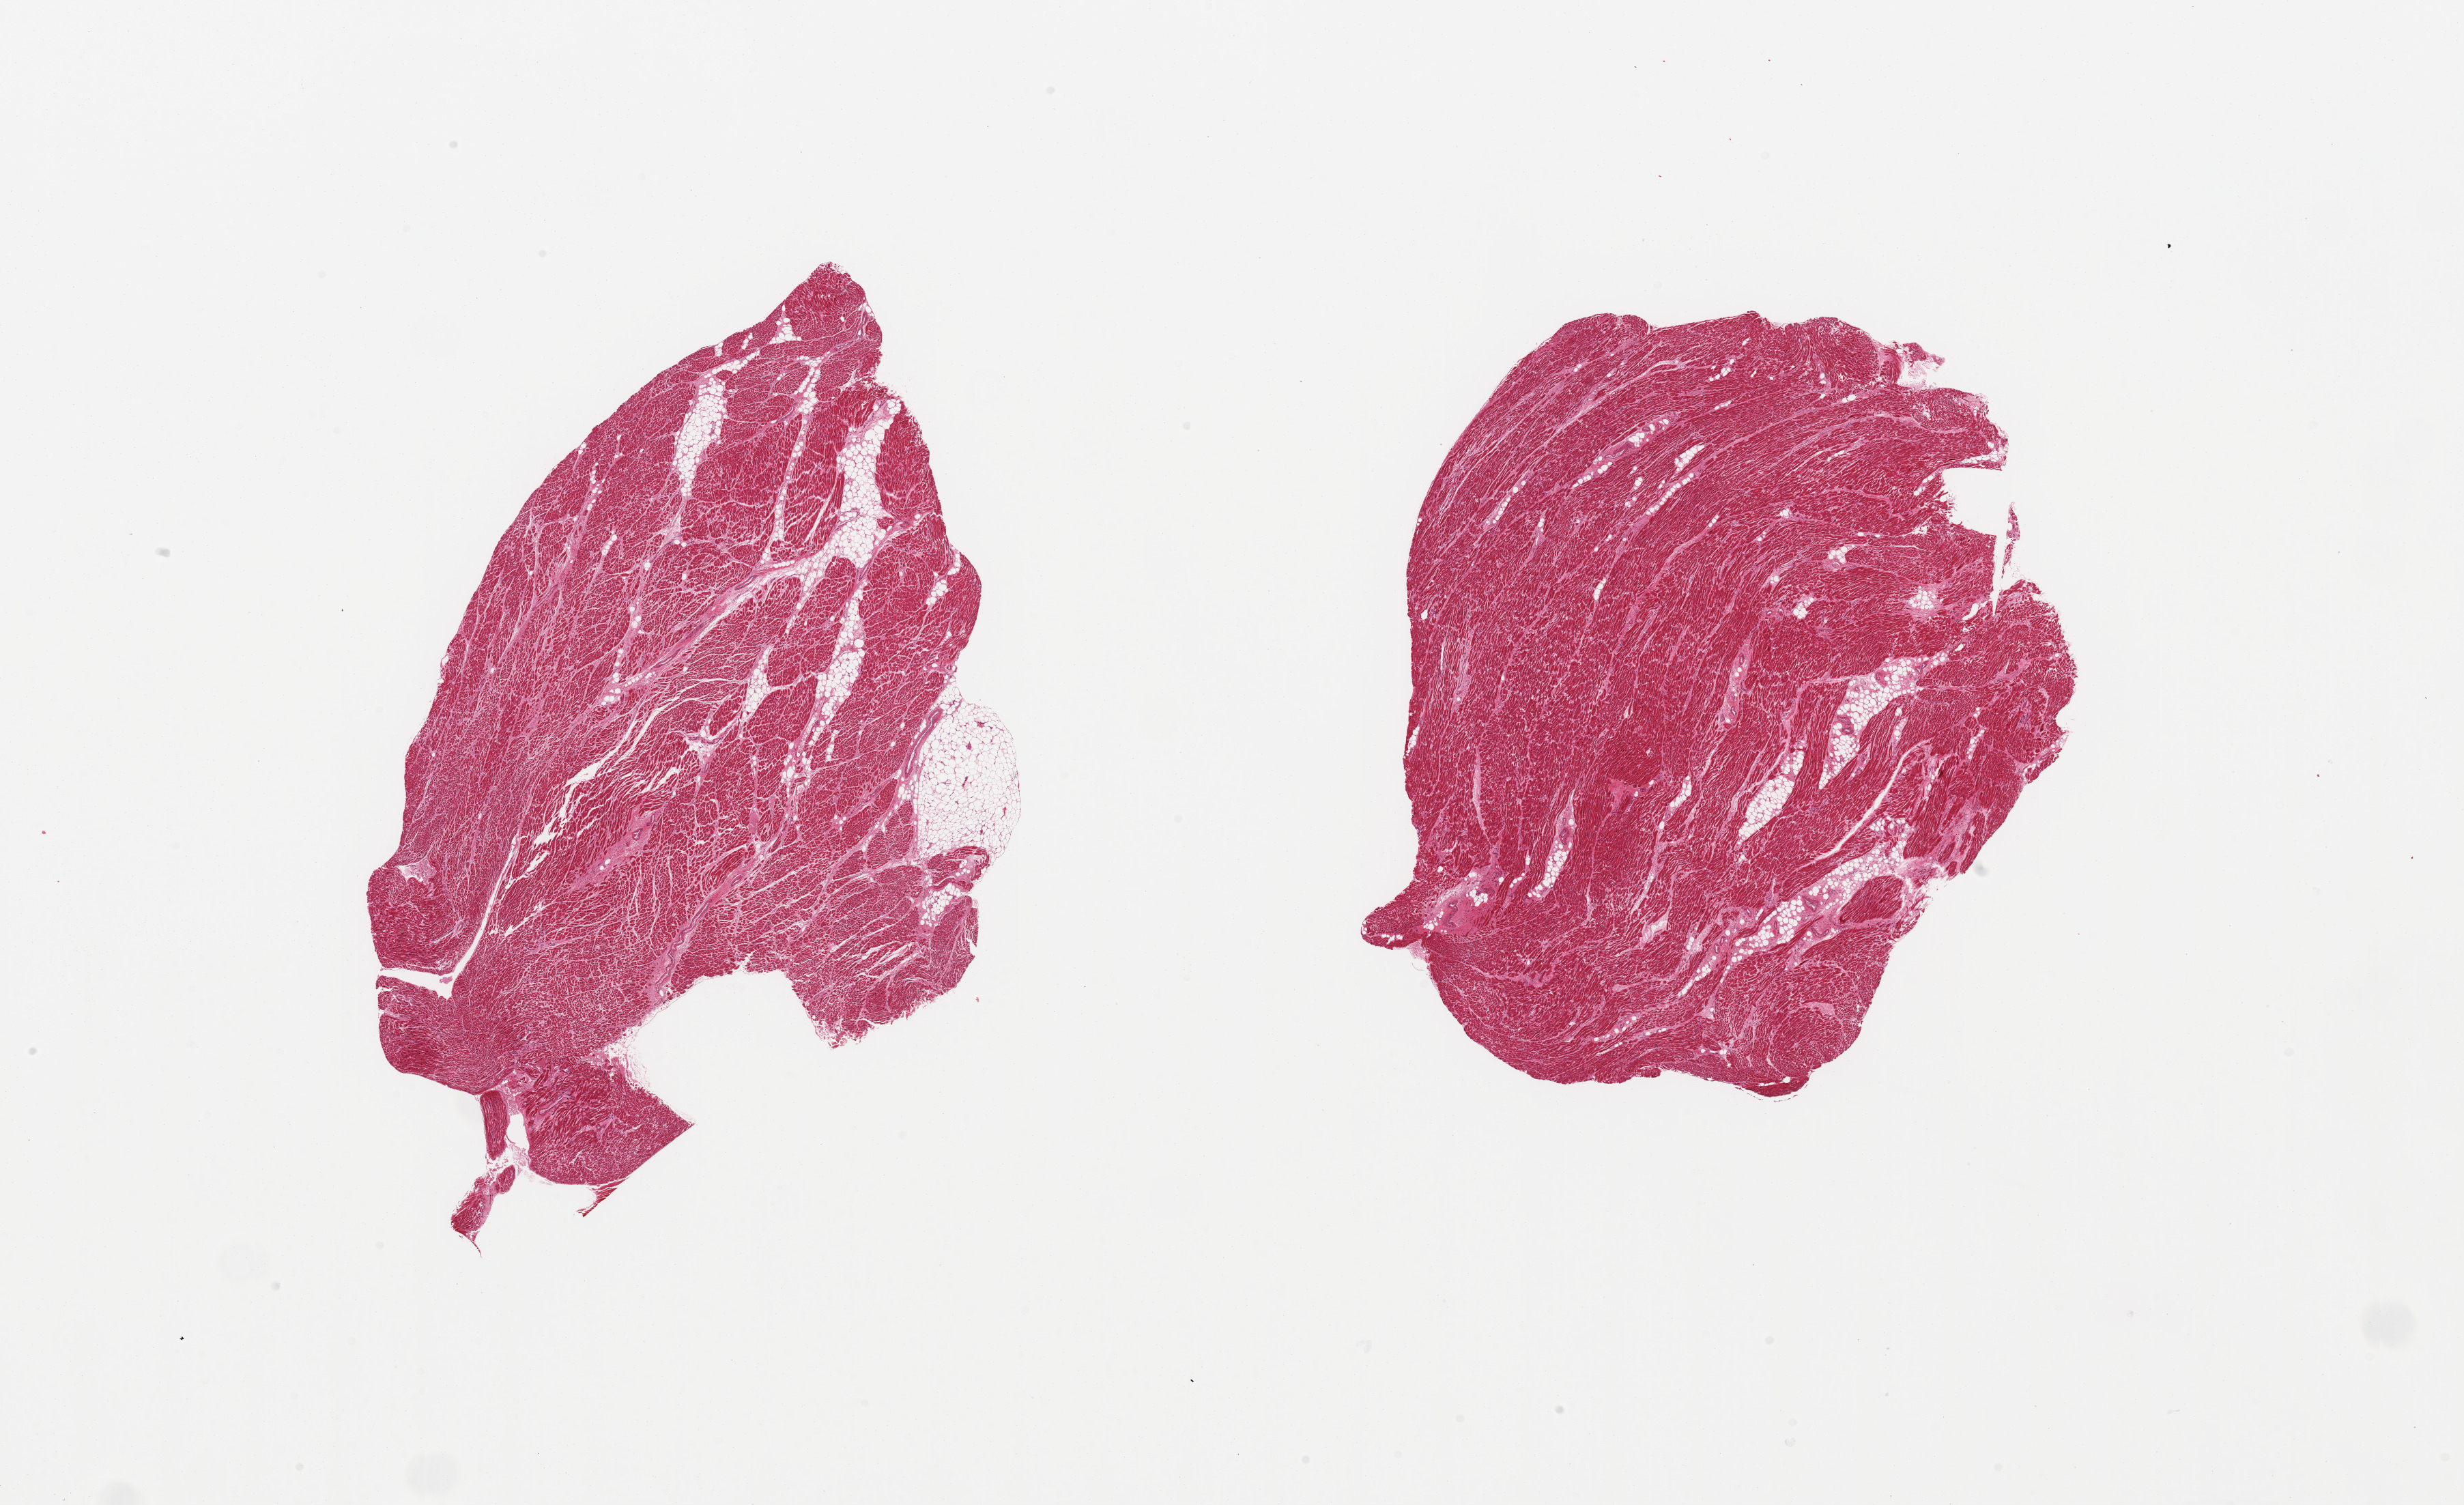
Digitized haematoxylin and eosin-stained section — a low-resolution overview of the entire scanned area, about 28.5 x 17.4 mm, PAXgene-fixed, paraffin-embedded tissue, target tissue: heart, tissue donor sample. Donor sex: male.
• pathologist's review note for this sample: 2 pieces, moderate interstitial fibrosis/chronic ischemic change